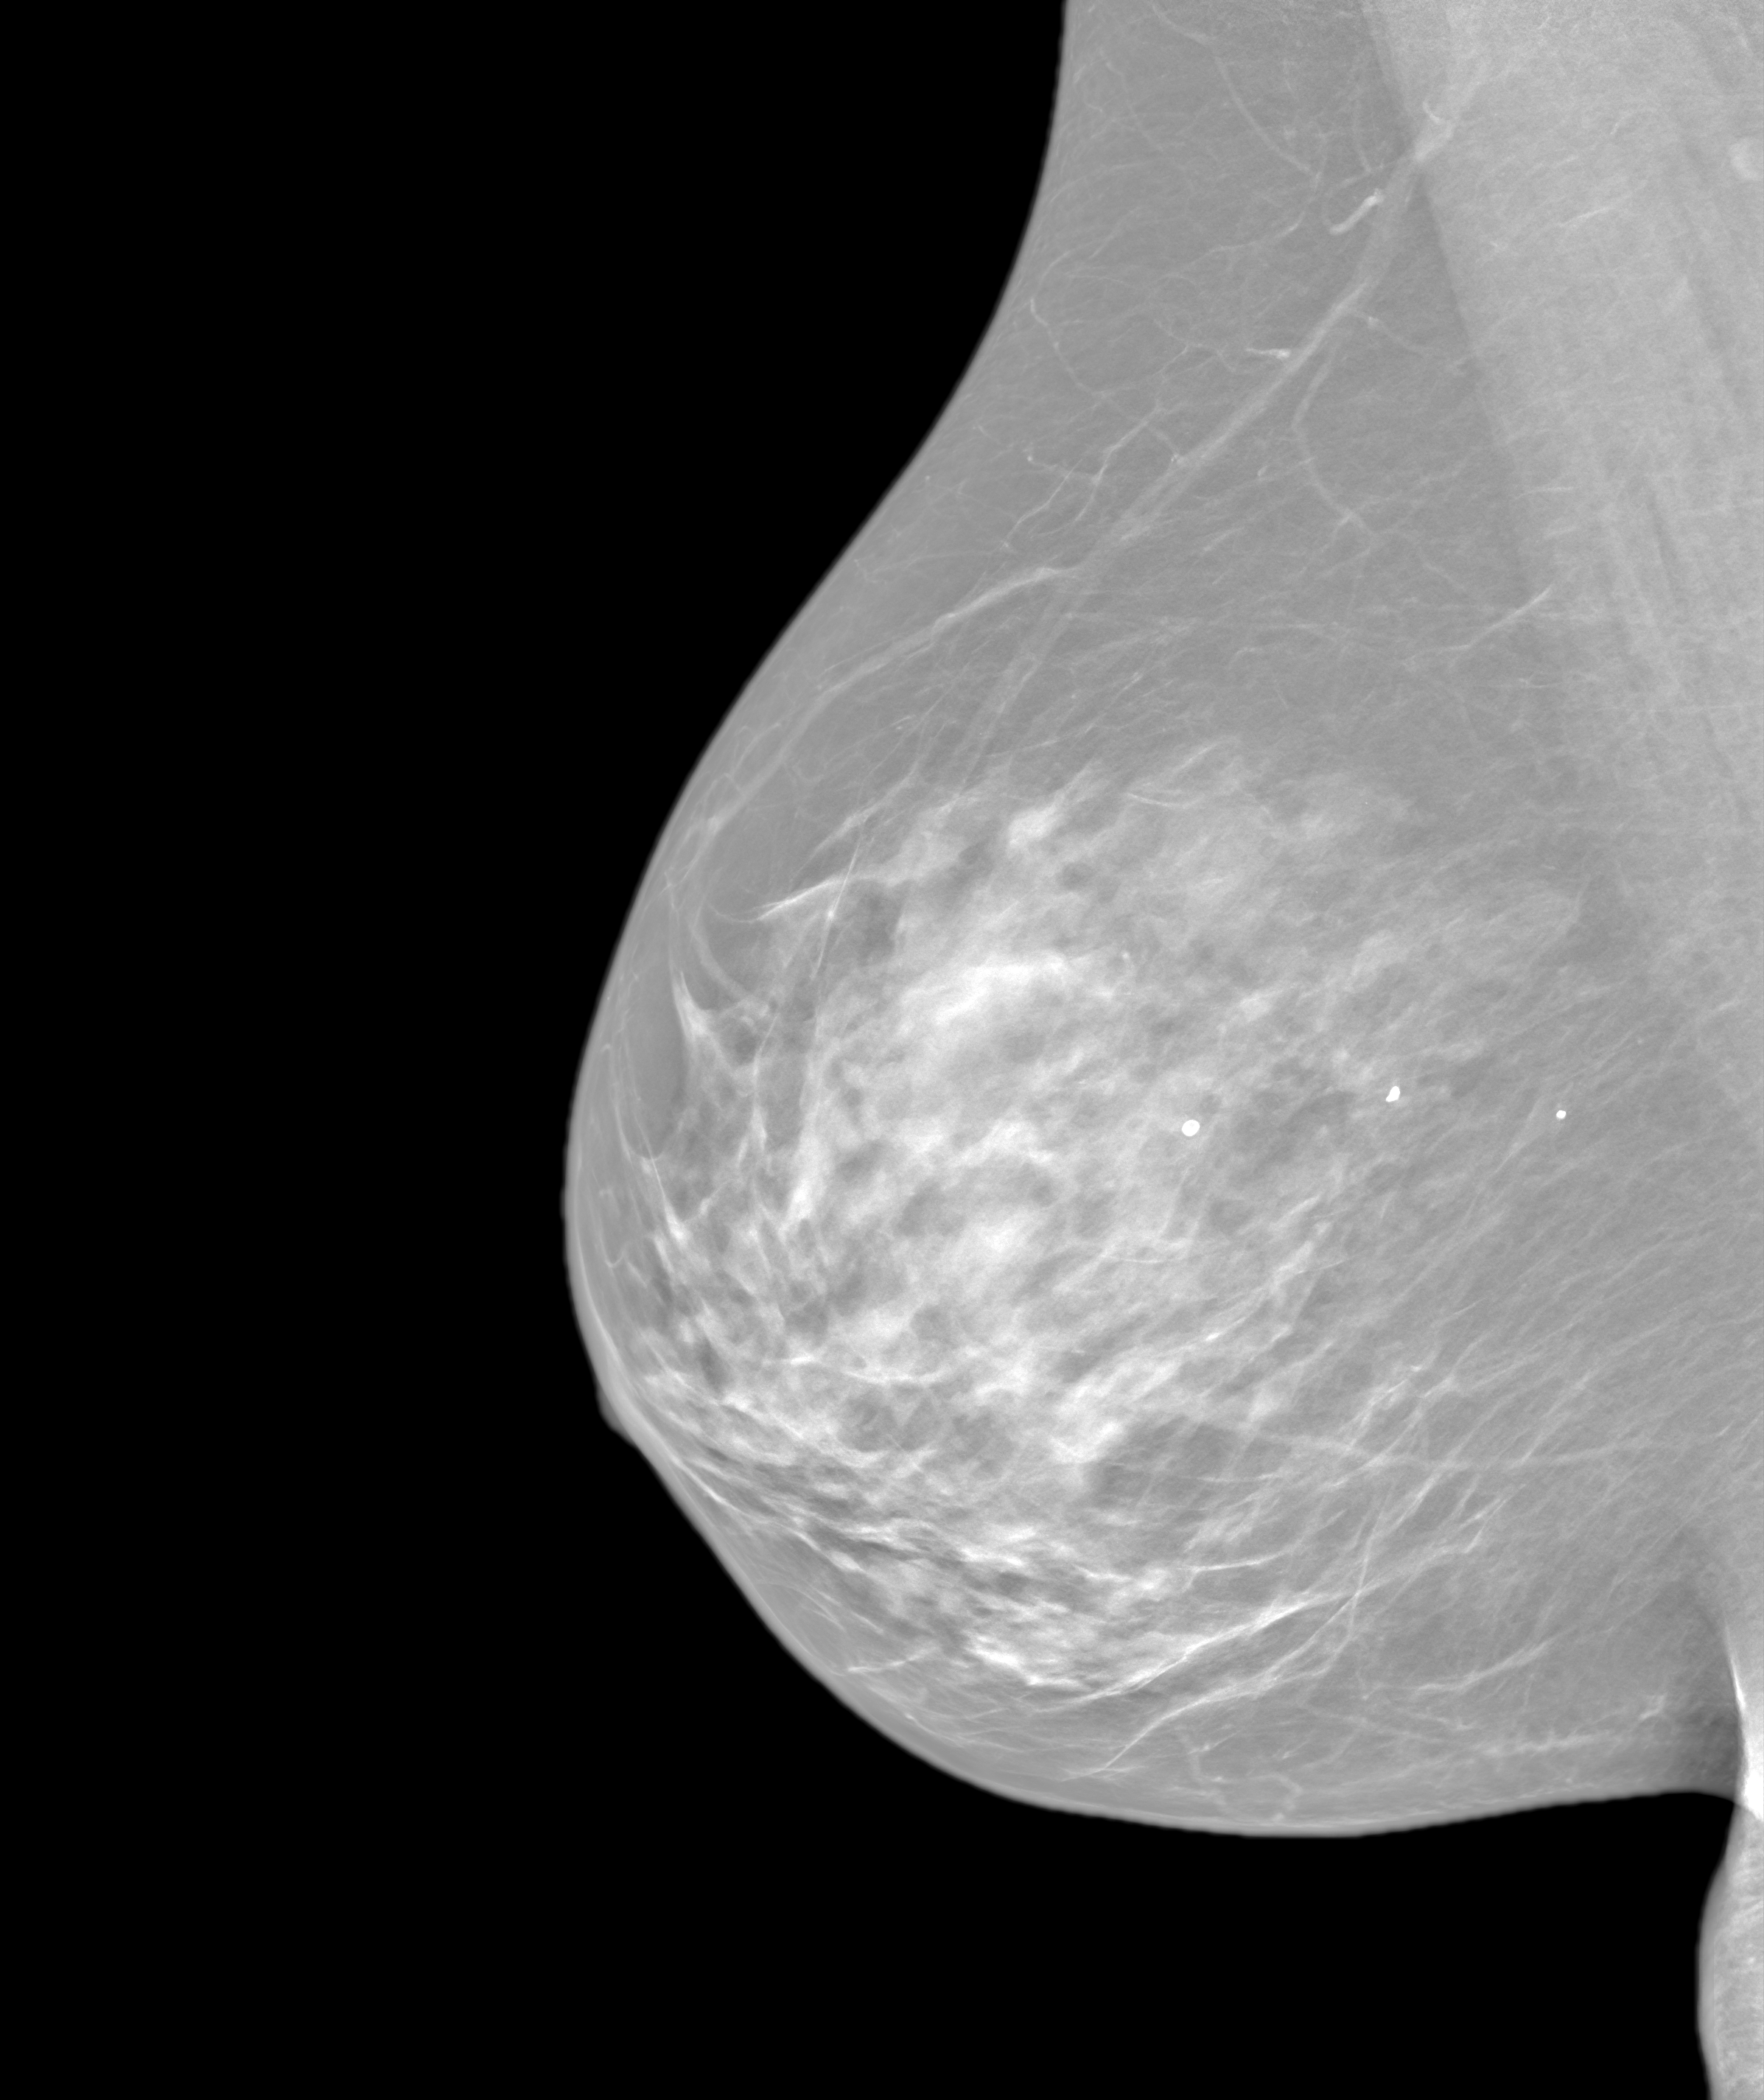
Screening examination. Patient: female, 66 years.
Image type: synthesized 2-D view from tomosynthesis. Breast: right. Projection: MLO view.